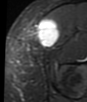
MRI of an extremity soft-tissue mass, one axial slice; position 15 of 48 along the scan axis; STIR; MR volume resampled by the dataset authors to the PET/CT grid (not the native acquisition matrix); 87 × 102 image matrix, field of view 85 × 100 mm. Female patient. Case-level facts recorded for this patient, not image findings: histological type: synovial sarcoma; grade: intermediate; site of the primary tumour: right thigh.
Structures marked on this image (expert contour drawn on MRI and transferred to this co-registered scan by the dataset authors):
- gross tumour volume including surrounding oedema: box from (x=37, y=20) to (x=59, y=48) px
- gross tumour volume (mass): (x=37, y=20)–(x=59, y=48)